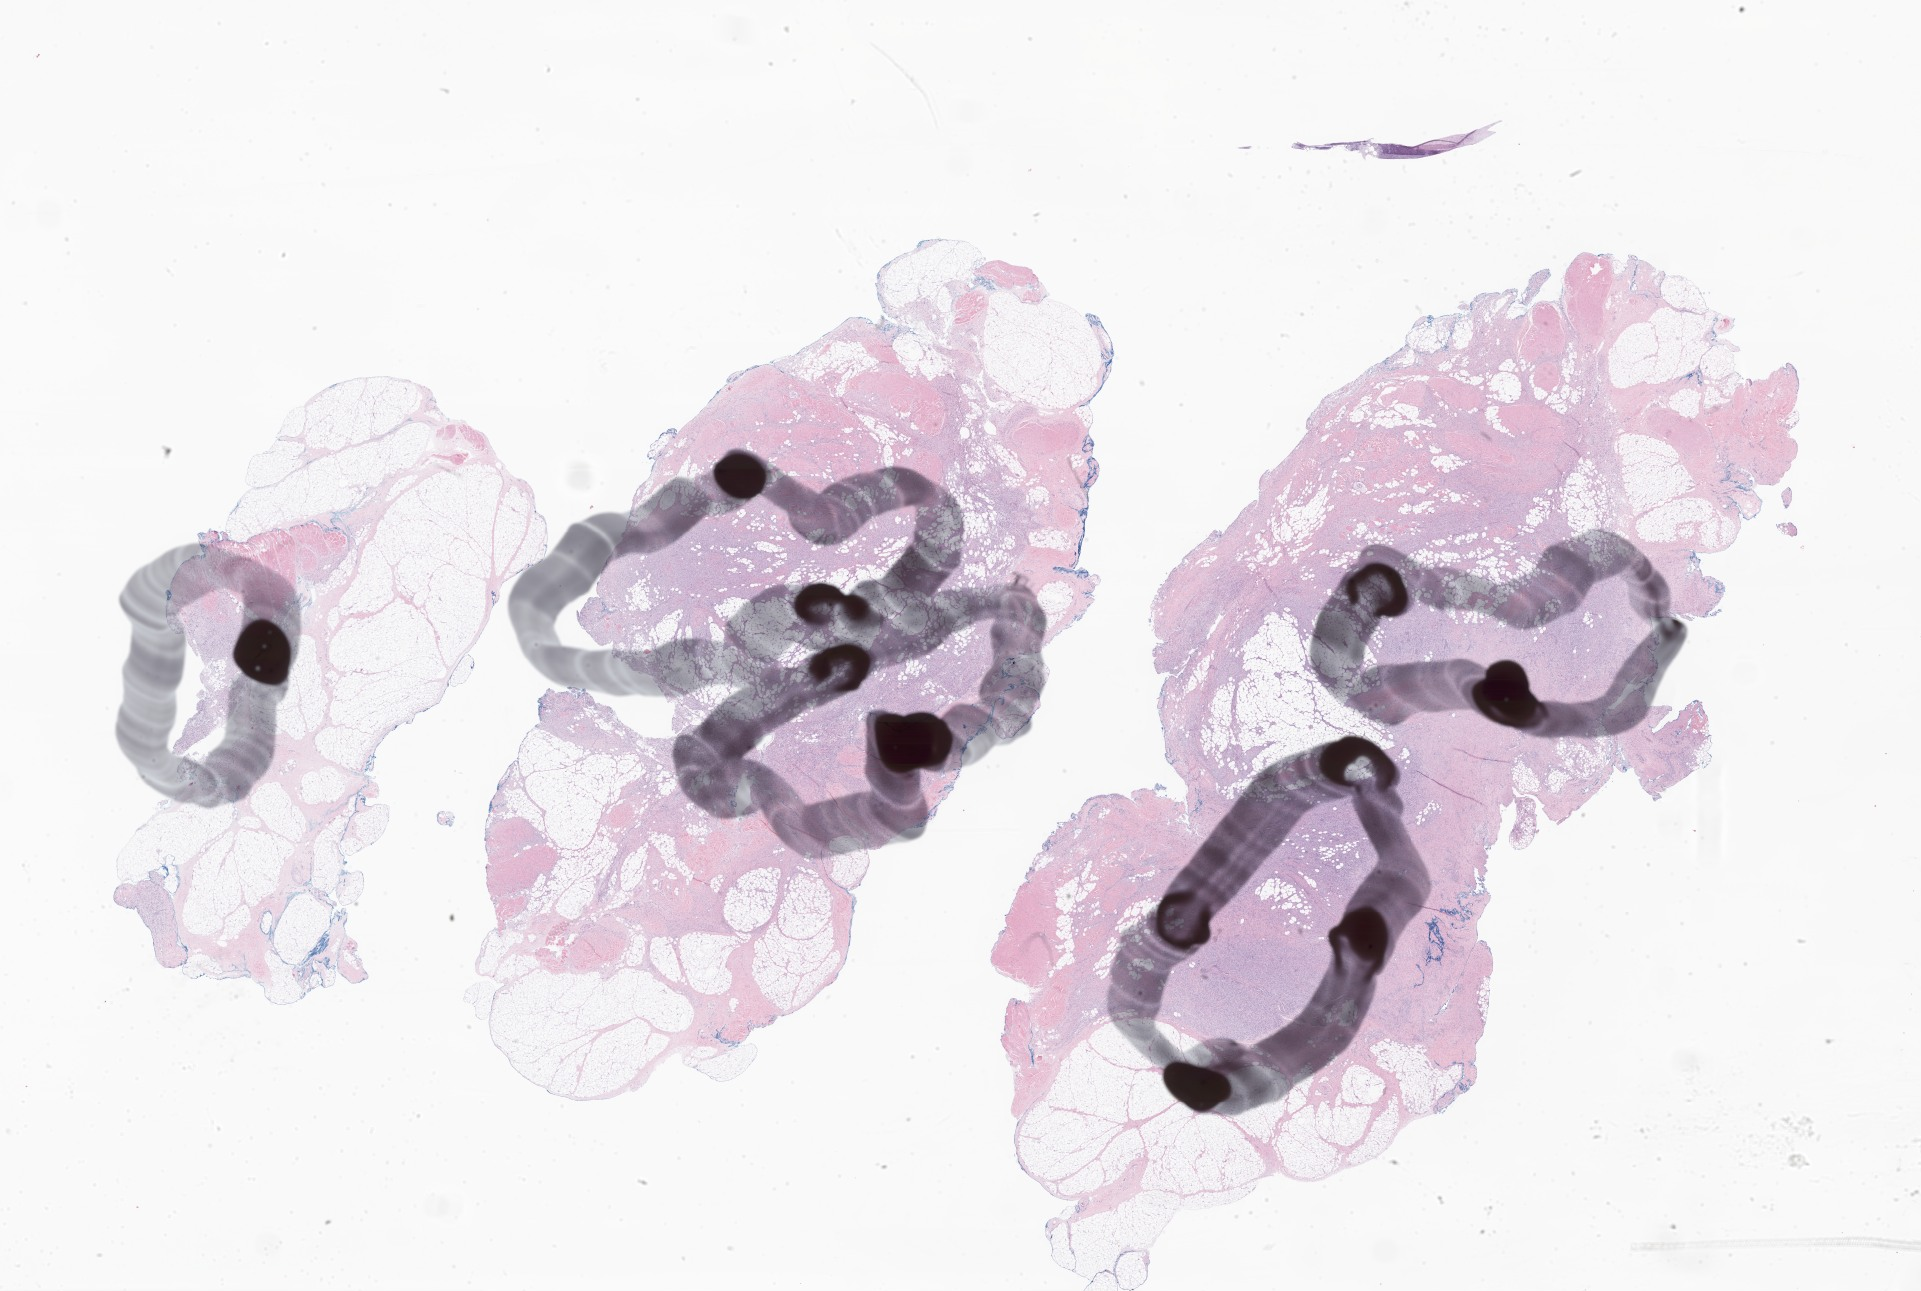
Haematoxylin and eosin whole-slide image of tumor tissue from the upper limb, a low-resolution overview of the entire scanned area, about 32.4 x 21.8 mm; formalin-fixed paraffin-embedded section. Male patient, age 76 months (6 years 4 months).
Diagnosis (ICD-O-3 morphology term): Malignant tumor, spindle cell type.